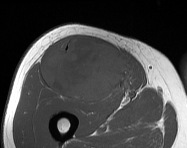
MRI of an extremity soft-tissue mass, one axial slice. Position 83 of 114 along the scan axis. MR volume resampled by the dataset authors to the PET/CT grid (not the native acquisition matrix). 3.27 mm slice thickness. 187 × 148 image matrix. Male patient. From the clinical record (not read from this slice): histological type: pleiomorphic leiomyosarcoma; grade: intermediate; site of the primary tumour: right thigh.
Structures marked on this image (expert contour drawn on MRI and transferred to this co-registered scan by the dataset authors):
- gross tumour volume including surrounding oedema: box from (x=43, y=36) to (x=133, y=103) px
- gross tumour volume (mass): (x=43, y=36)–(x=133, y=103)